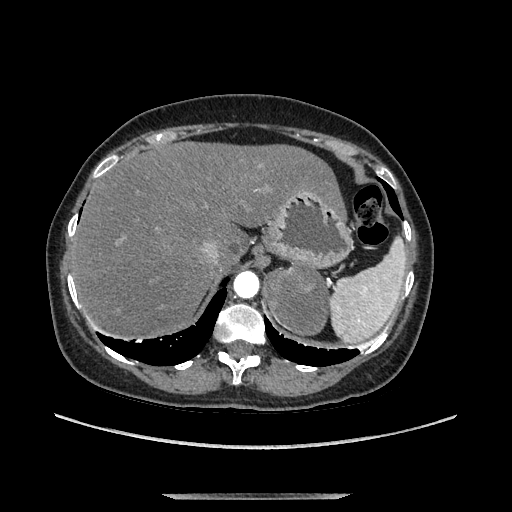
Contrast-enhanced abdominal CT, one axial slice. Slice 107 of 169 in the series (ordered by position). Soft-tissue window (W 400 / L 40 HU). 1.25 mm slice thickness. 512 × 512 image matrix, field of view 400 × 400 mm. Female patient. Case-level facts recorded for this patient, not image findings: diagnosis: adrenocortical carcinoma; tumour side: left adrenal; tumour size at pathology: 9 cm; Ki-67 index: 2 %; stage (as recorded): 3.
Structures marked on this image (semi-automatically segmented with operator editing):
- mass: bounding box <267,267,326,334> (left, top, right, bottom; pixels)